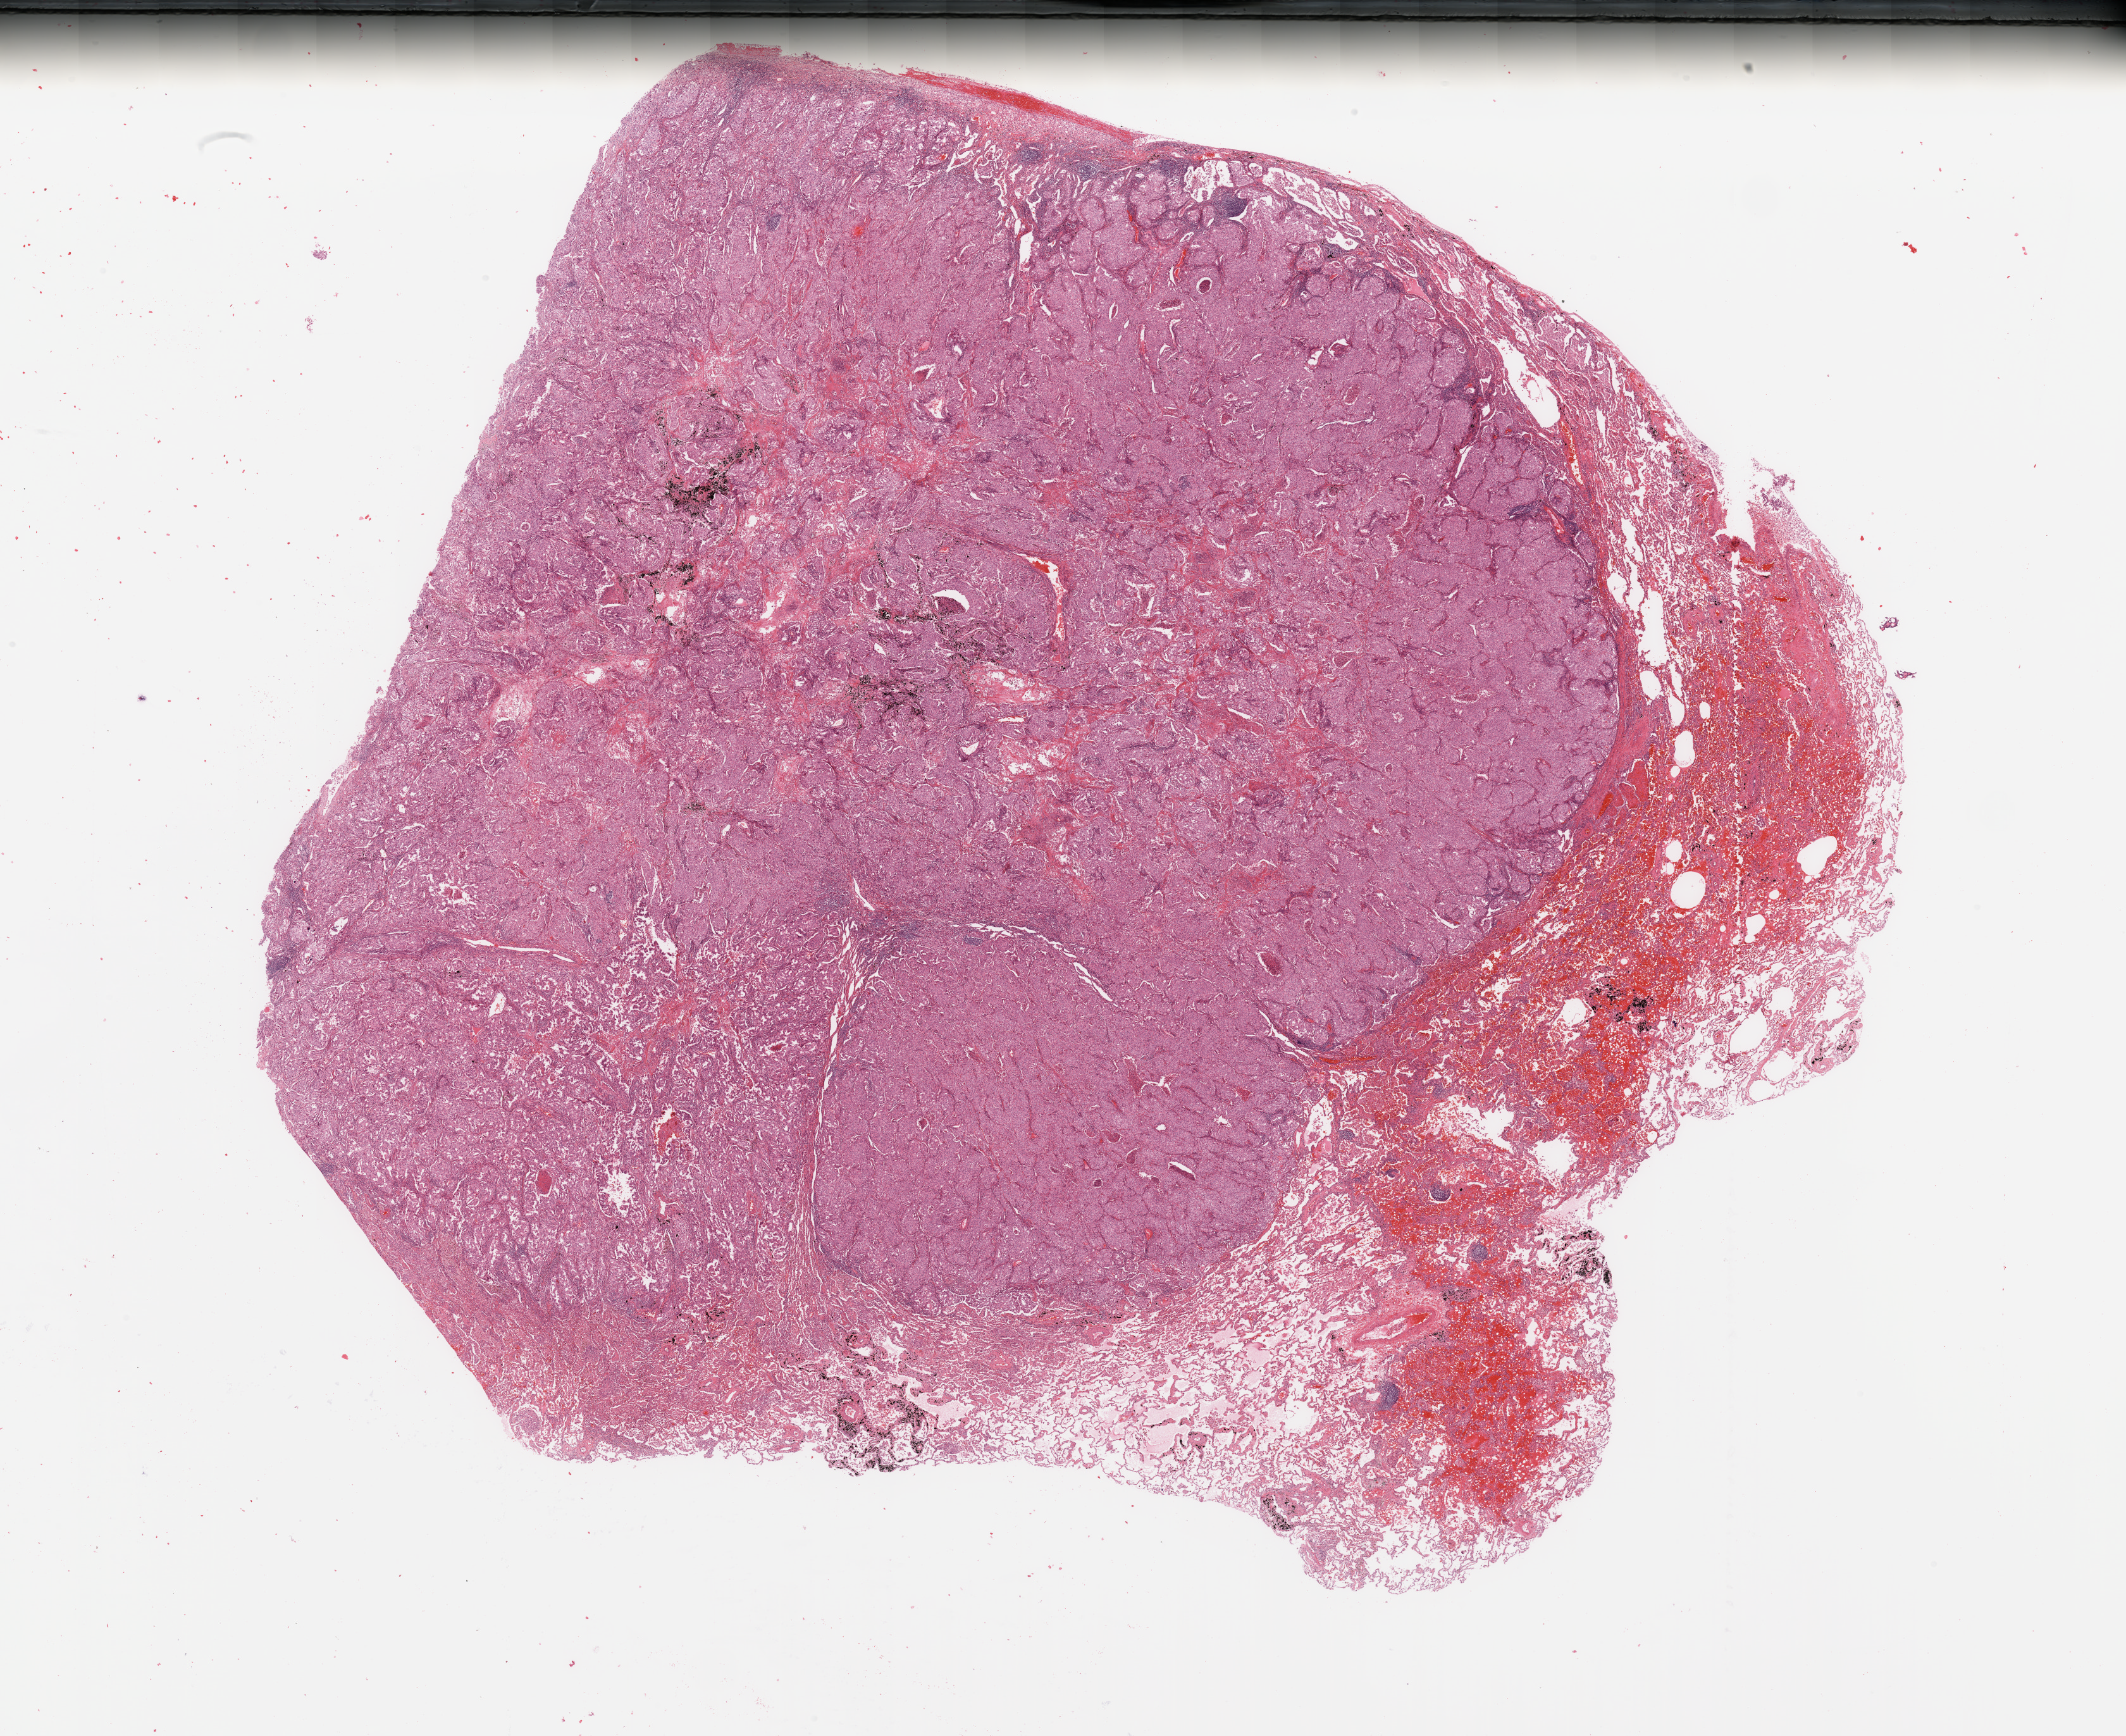
H&E whole-slide image, a low-resolution overview of the entire scanned area, about 26.6 x 21.7 mm (acquisition: 20x scan), tumour tissue sample, lung. 56-year-old male patient. Histologic grade: G3 (poorly differentiated).
Diagnosis: Adenocarcinoma, NOS. AJCC pathologic stage: IB.